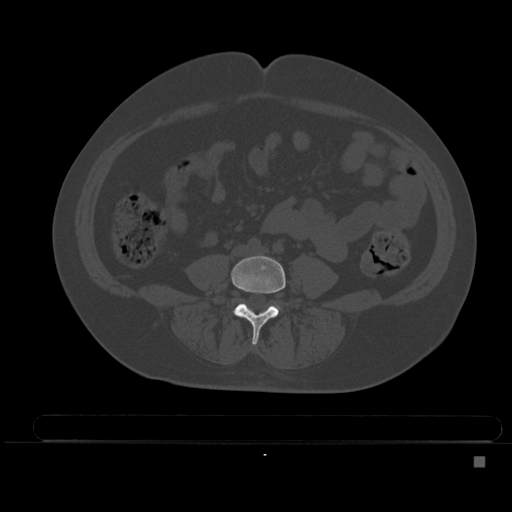
CT including the spine, one axial slice. Position 125 of 495 along the scan axis. Bone window (W 1800 / L 400 HU). 1.5 mm slice thickness. 512 × 512 image matrix, field of view 404 × 404 mm. Female patient, age 33 years. From the clinical record (not read from this slice): primary cancer: breast; vertebrae with lytic lesions (as recorded): T1.
Structures marked on this image (semi-automatic segmentation, software-assisted and operator-edited):
- L4 vertebra: bounding box <231,255,286,345> (left, top, right, bottom; pixels)